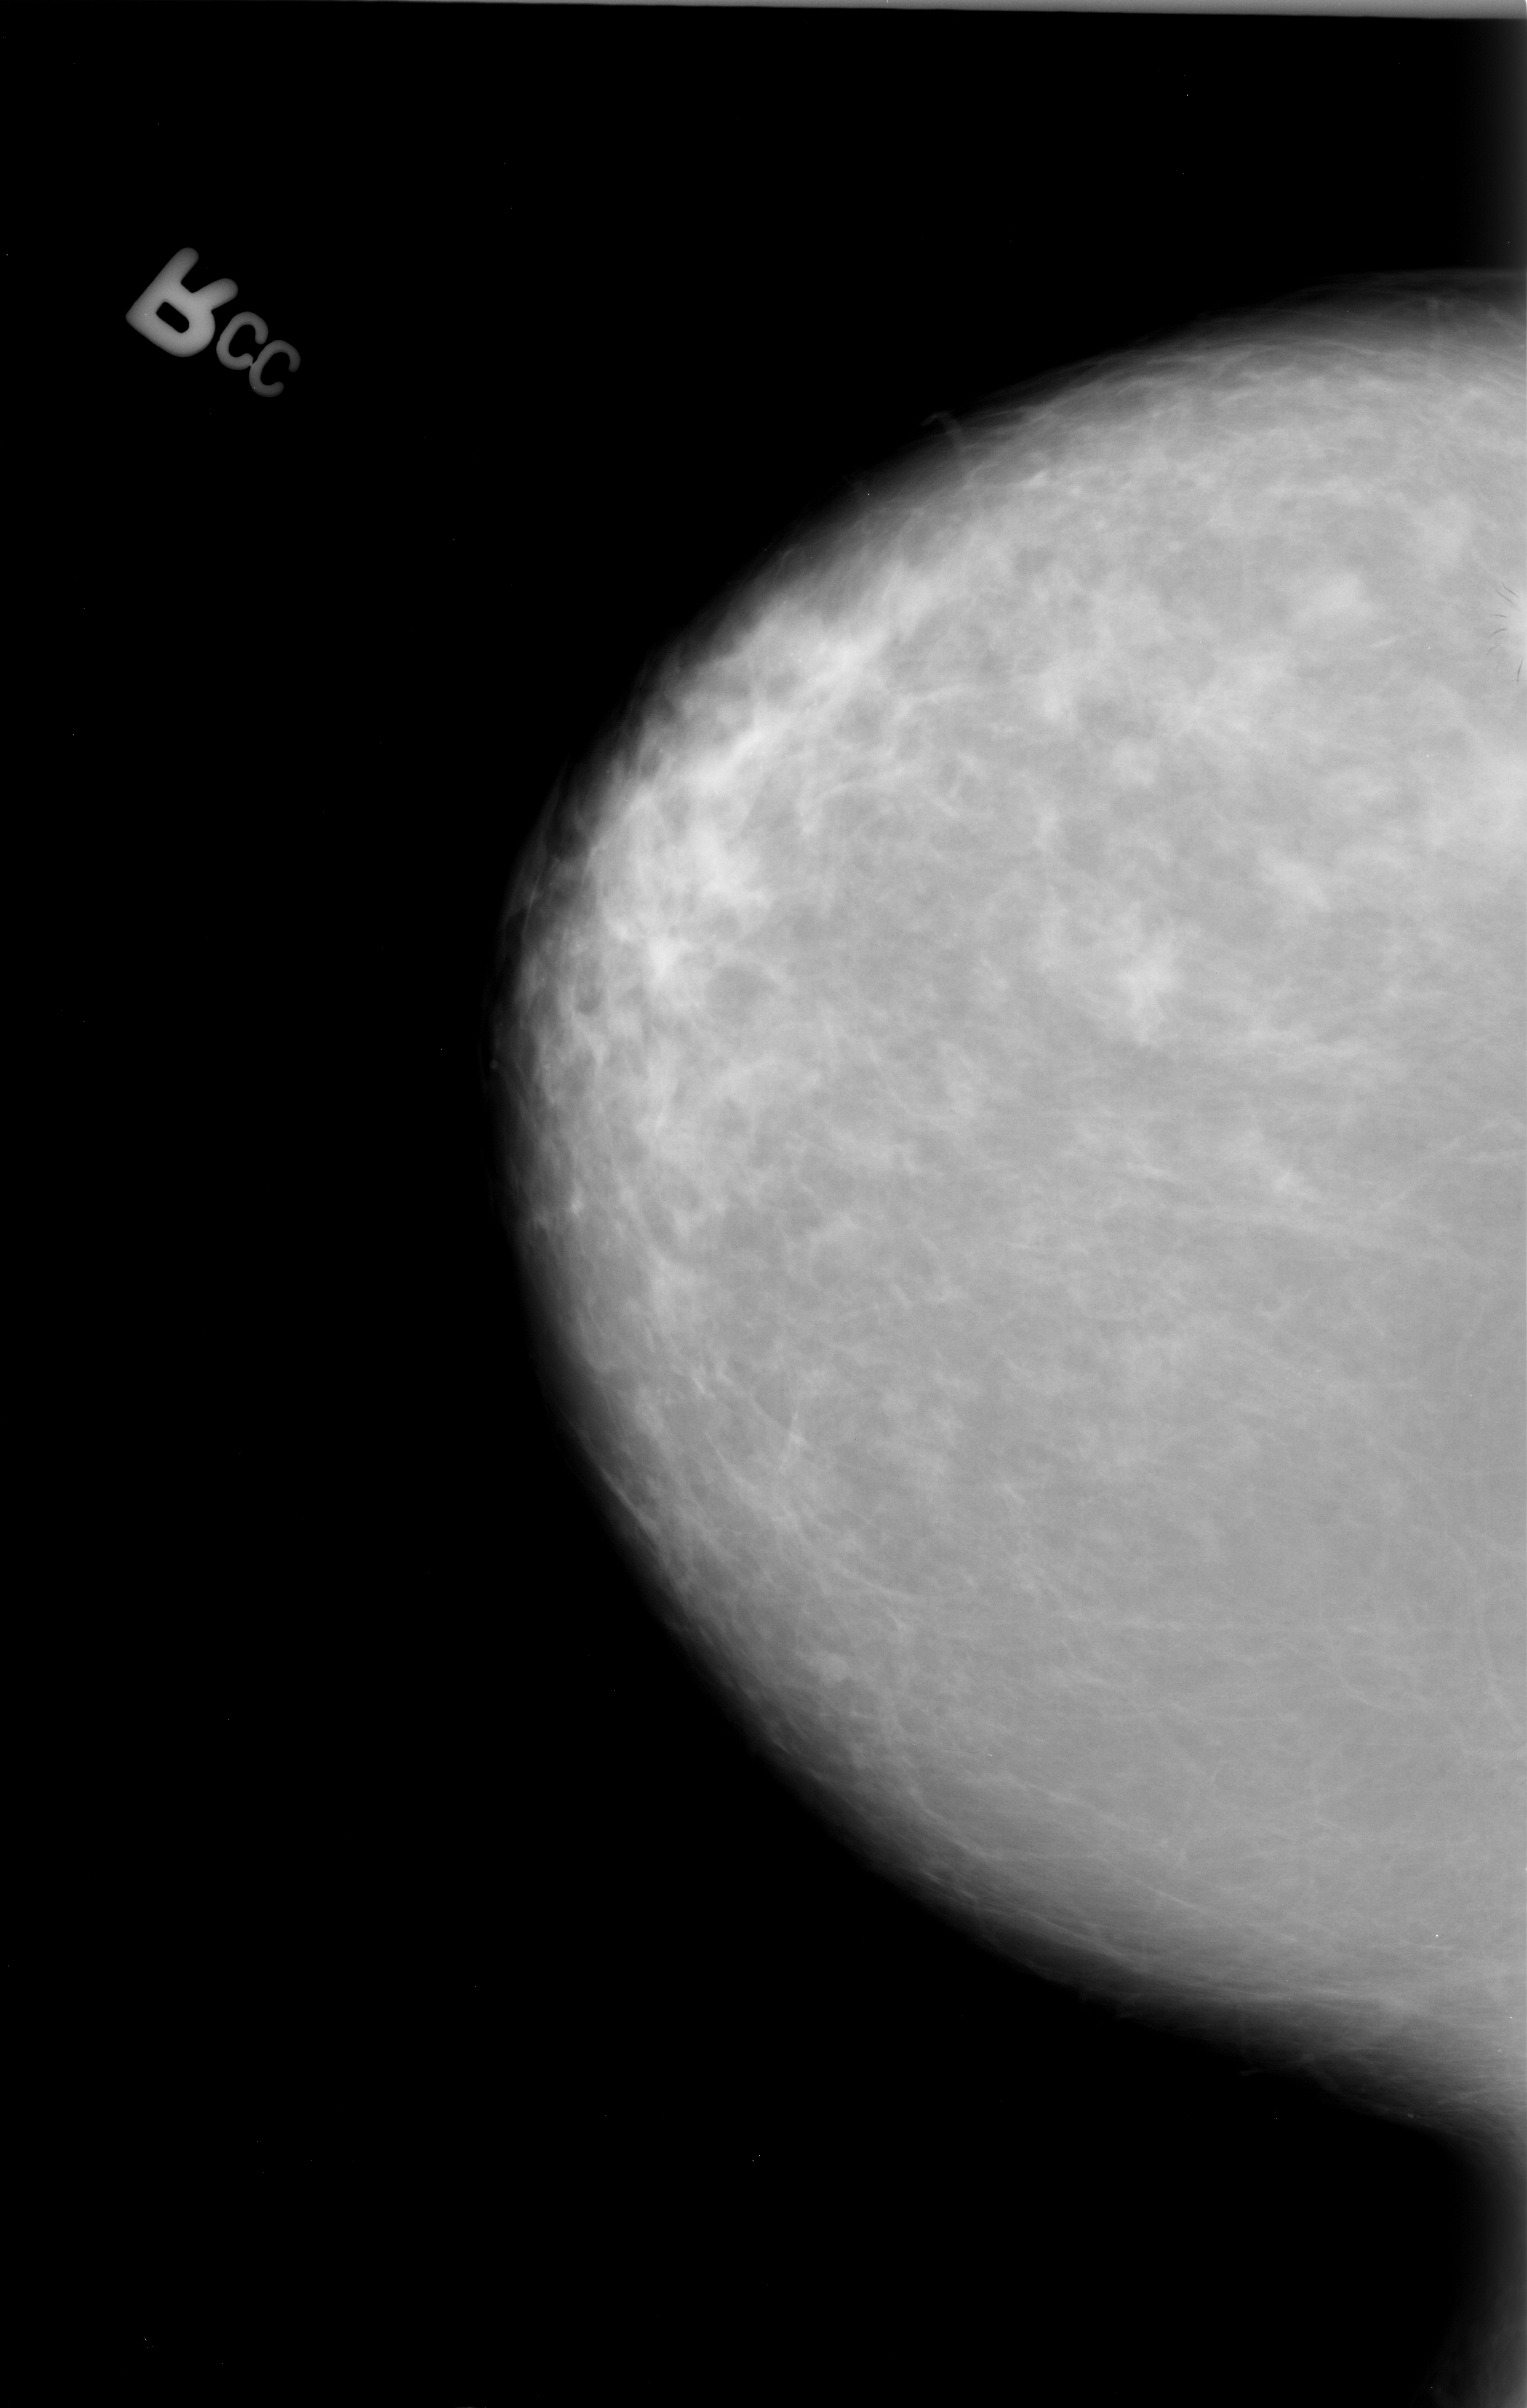
Mammogram (digitized film), right breast, craniocaudal (CC) view, breast composition: scattered fibroglandular densities (BI-RADS density category 2 of 4).
- Abnormality record for this image: mass, shape architectural distortion, margins spiculated; BI-RADS assessment category 4; subtlety rating 2 on a 1 (subtle) to 5 (obvious) scale; pathology result (as recorded, not read from the image): malignant.